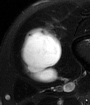
MRI of an extremity soft-tissue mass, one axial slice. Slice 20 of 65 in the series (ordered by position). T2-weighted fat-saturated. MR volume resampled by the dataset authors to the PET/CT grid (not the native acquisition matrix). 3.27 mm slice thickness. 90 × 105 image matrix, field of view 88 × 103 mm. Male patient. Case-level facts recorded for this patient, not image findings: histological type: mixoid liposarcoma; grade: low; site of the primary tumour: left thigh.
Structures marked on this image (expert contour drawn on MRI and transferred to this co-registered scan by the dataset authors):
- gross tumour volume (mass): bounding box (x1, y1, x2, y2) in pixels: (20, 25, 62, 83)